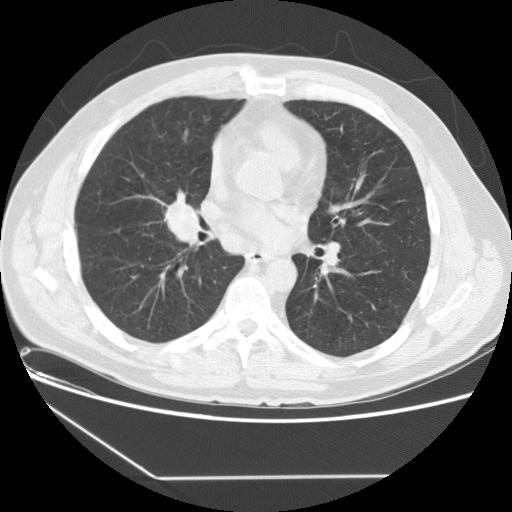
Low-dose screening chest CT, one axial slice; slice 76 of 154 in the series (ordered by position); reconstruction kernel STANDARD; 120 kVp; lung window (W 1500 / L -600 HU); 512 × 512 image matrix, field of view 370 × 370 mm.
Annotated regions visible in this slice (expert manual segmentation):
- lesion 1 (tumor, middle lobe of right lung): box from (x=167, y=202) to (x=200, y=240) px